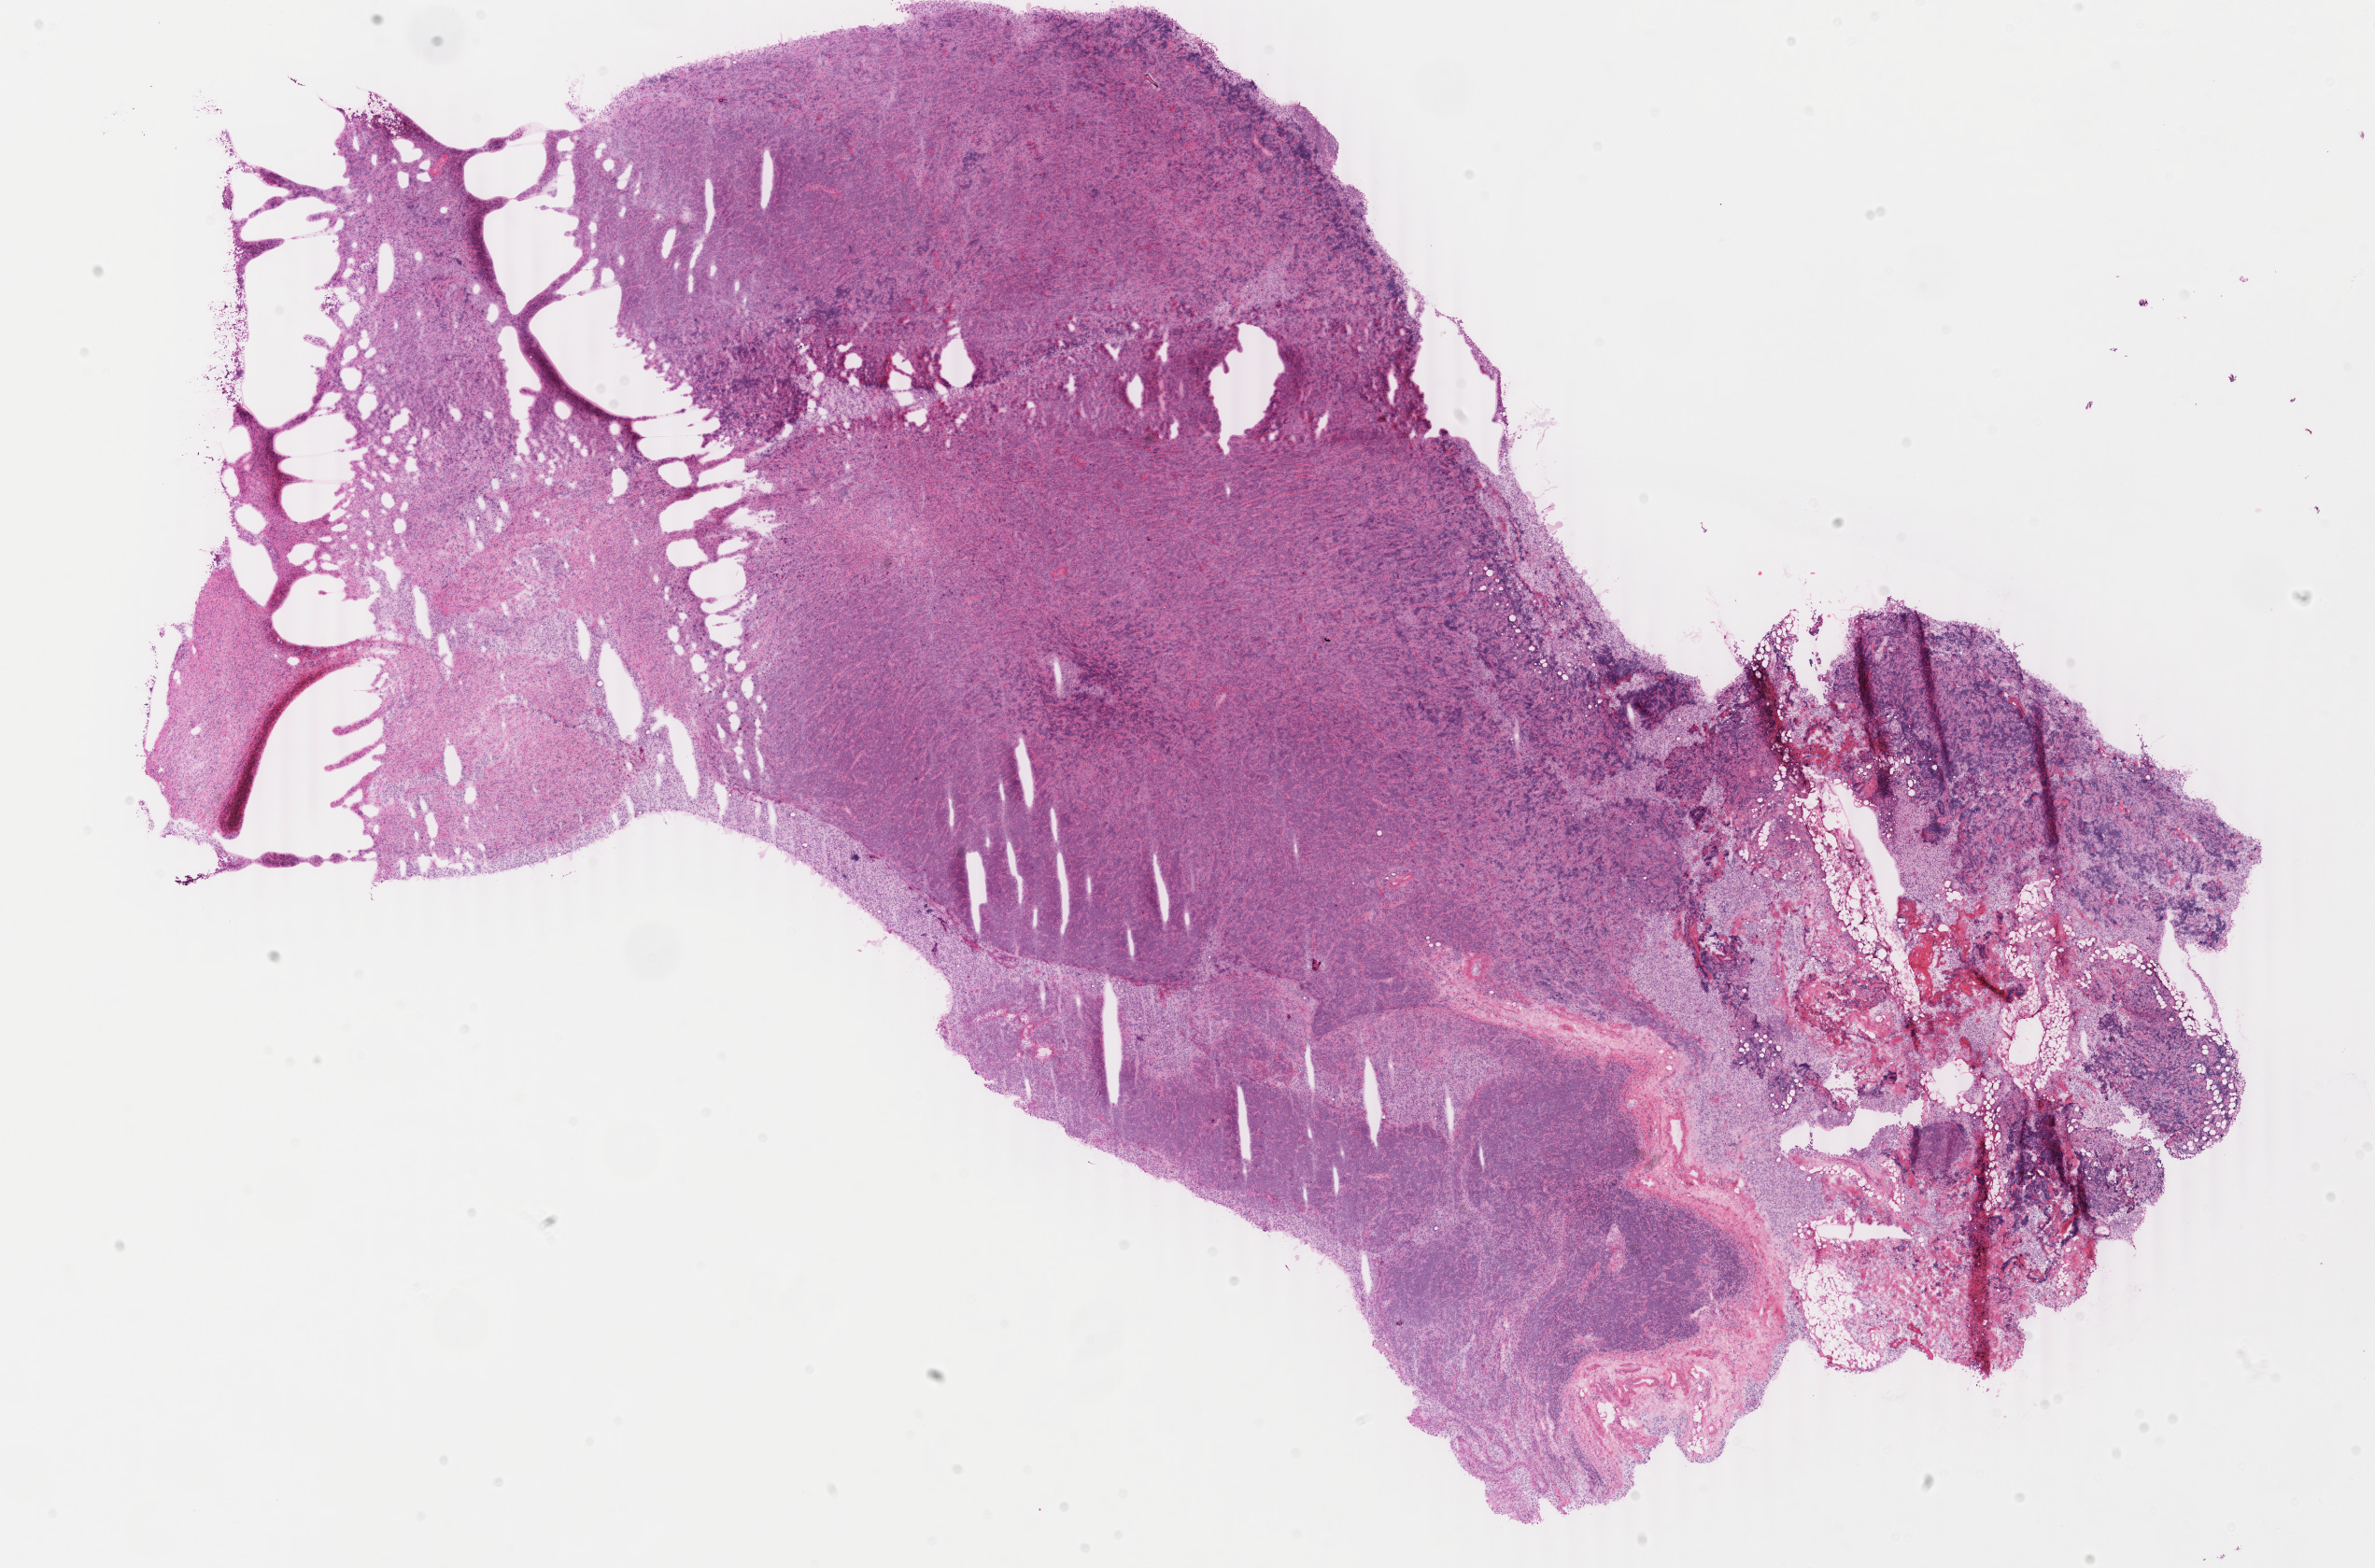
Whole-slide histology image, H&E-stained — shown as a low-resolution overview of the whole scanned area (about 20.2 x 13.4 mm, acquisition: 40x scan). Frozen section from the top of the tissue portion. Lymphoid tissue, primary tumour sample. Female, age 66 years at initial diagnosis. Slide review estimates, as recorded: tumour cells 90%, tumour nuclei 95%, normal cells 3%, stromal cells 5%, necrosis 2%. Infiltration values recorded for this section: lymphocyte infiltration 3%, monocyte infiltration 0%, neutrophil infiltration 0%.
* diagnosis: Diffuse large B-cell lymphoma, NOS (lymph nodes of head, face and neck)